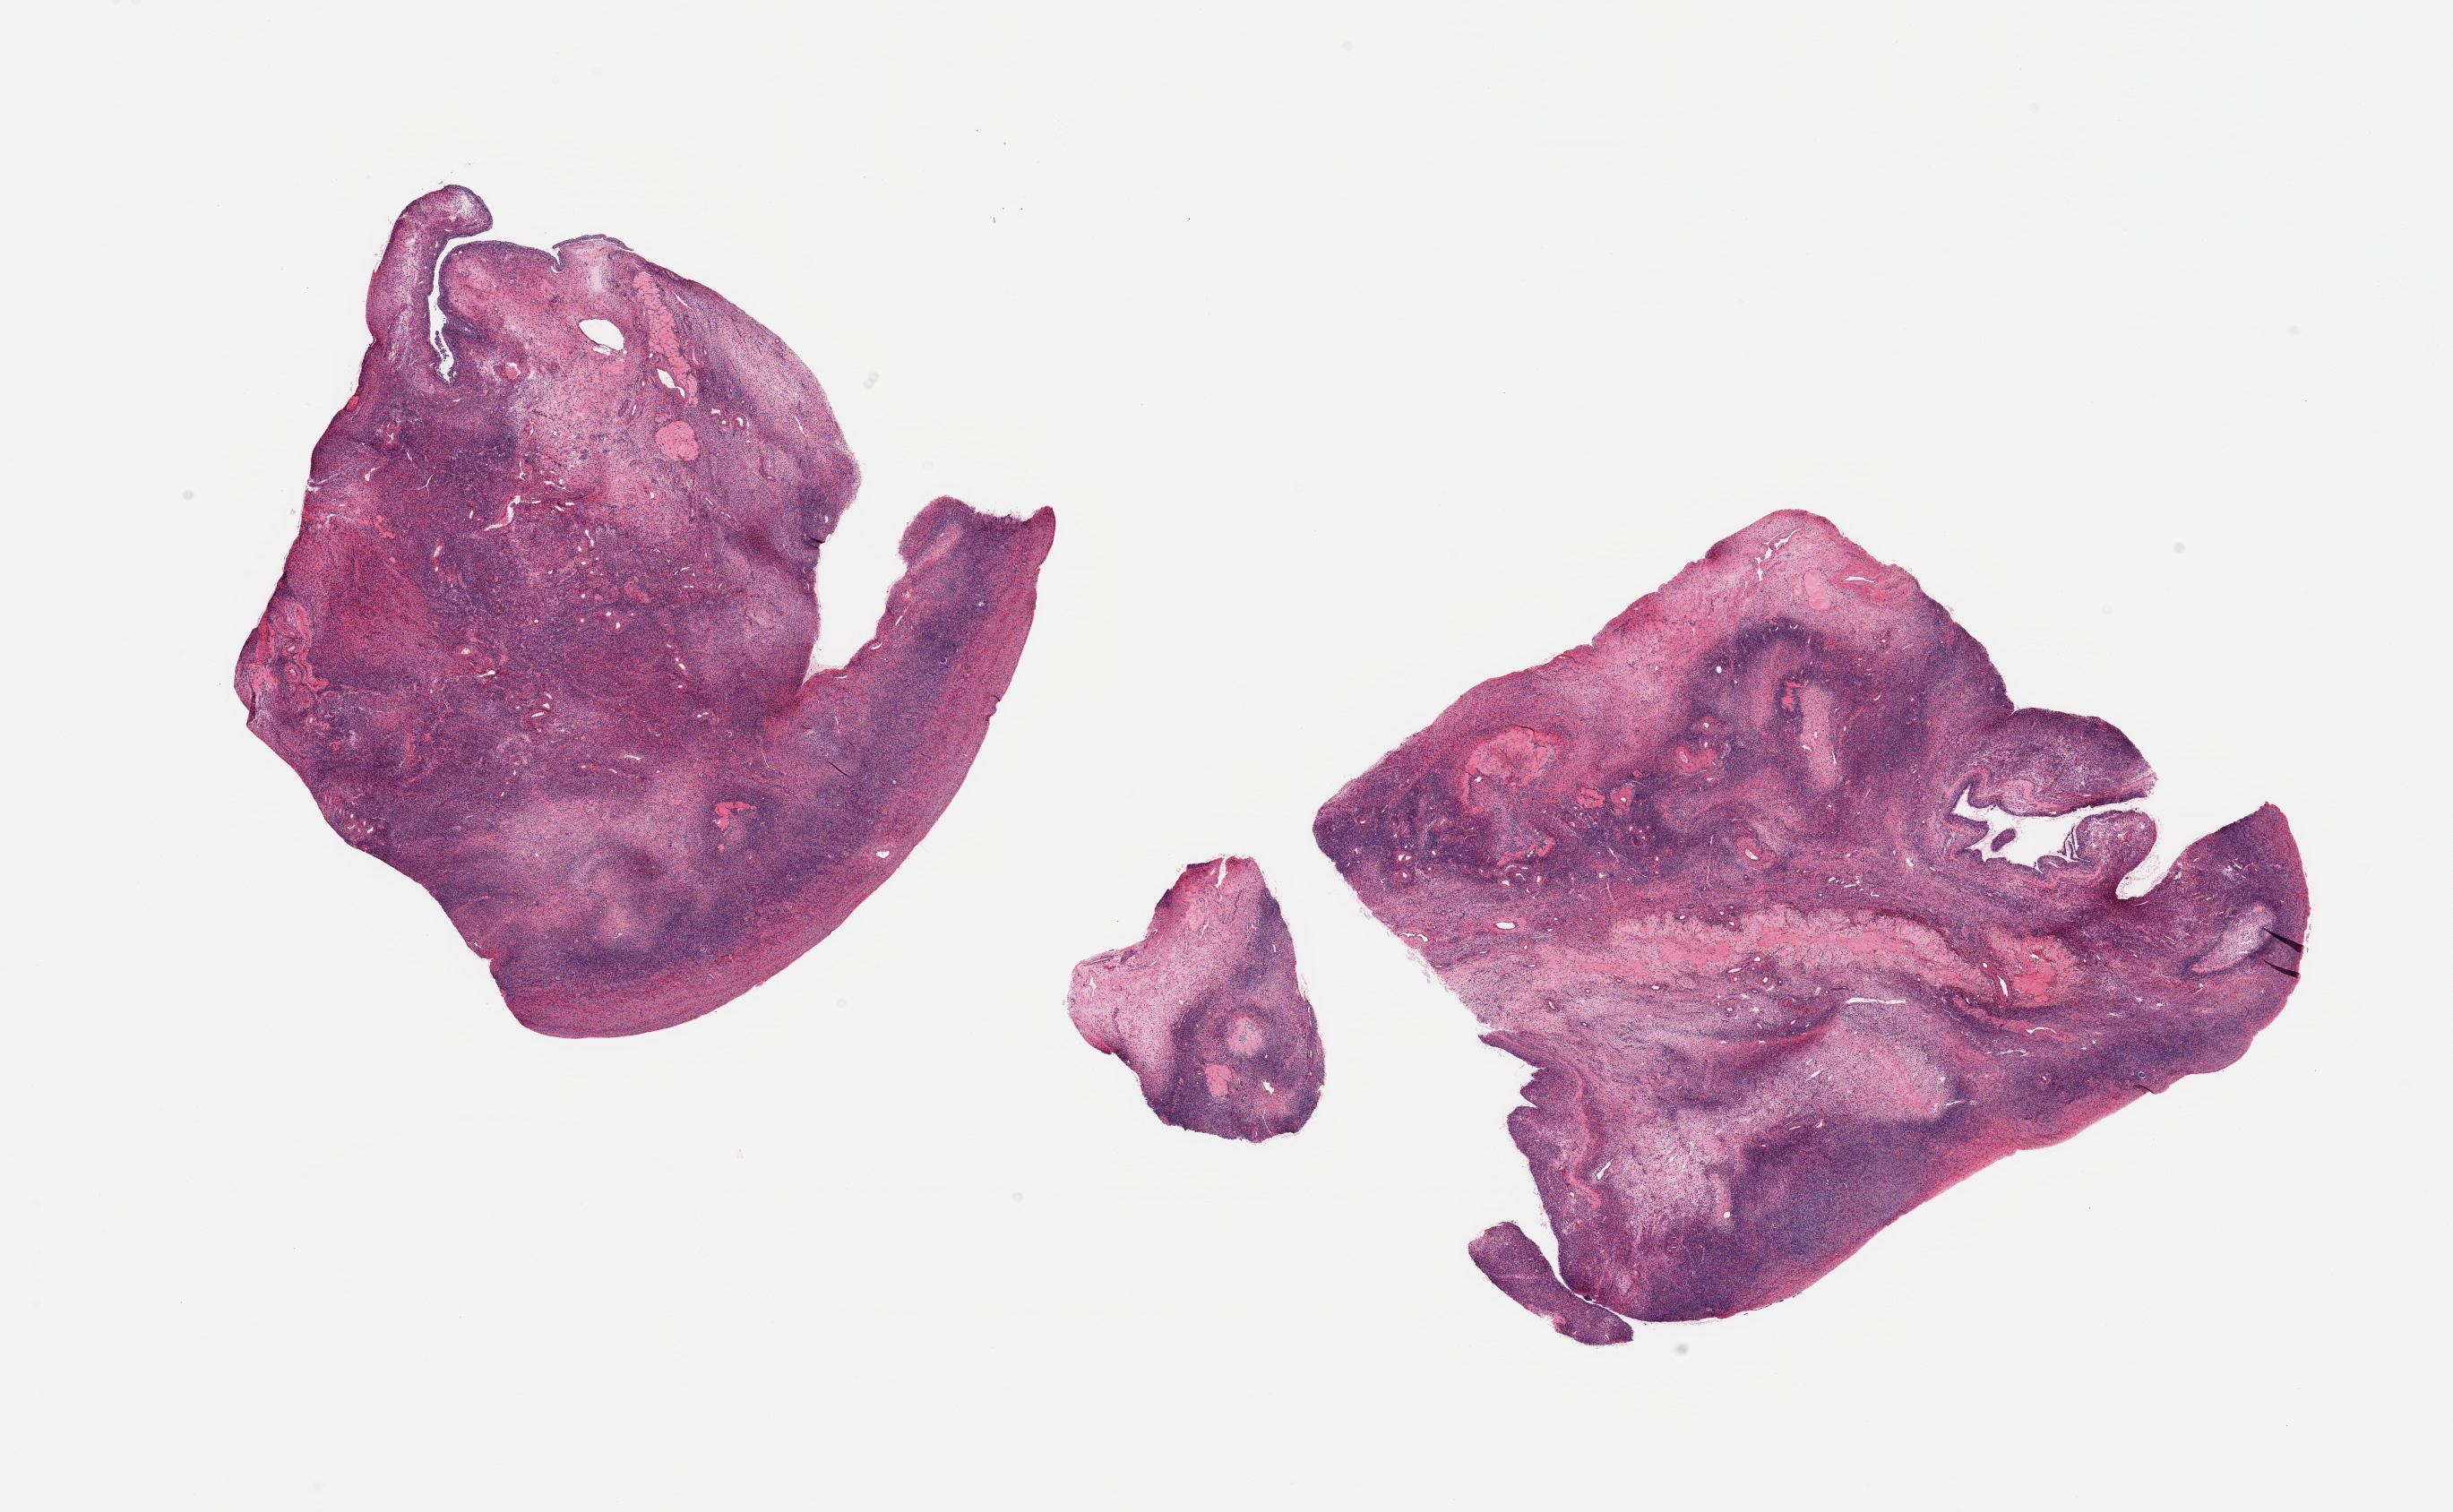
Digitized H&E-stained section — whole scanned area (about 21.7 x 13.4 mm, slide scanned at 20x) shown as a low-resolution overview. PAXgene-fixed paraffin-embedded (PFPE) section. Section of ovary (target tissue). Donor tissue sample.
- pathologist's review note for this sample: 2 pieces; ova & corpora in various stages